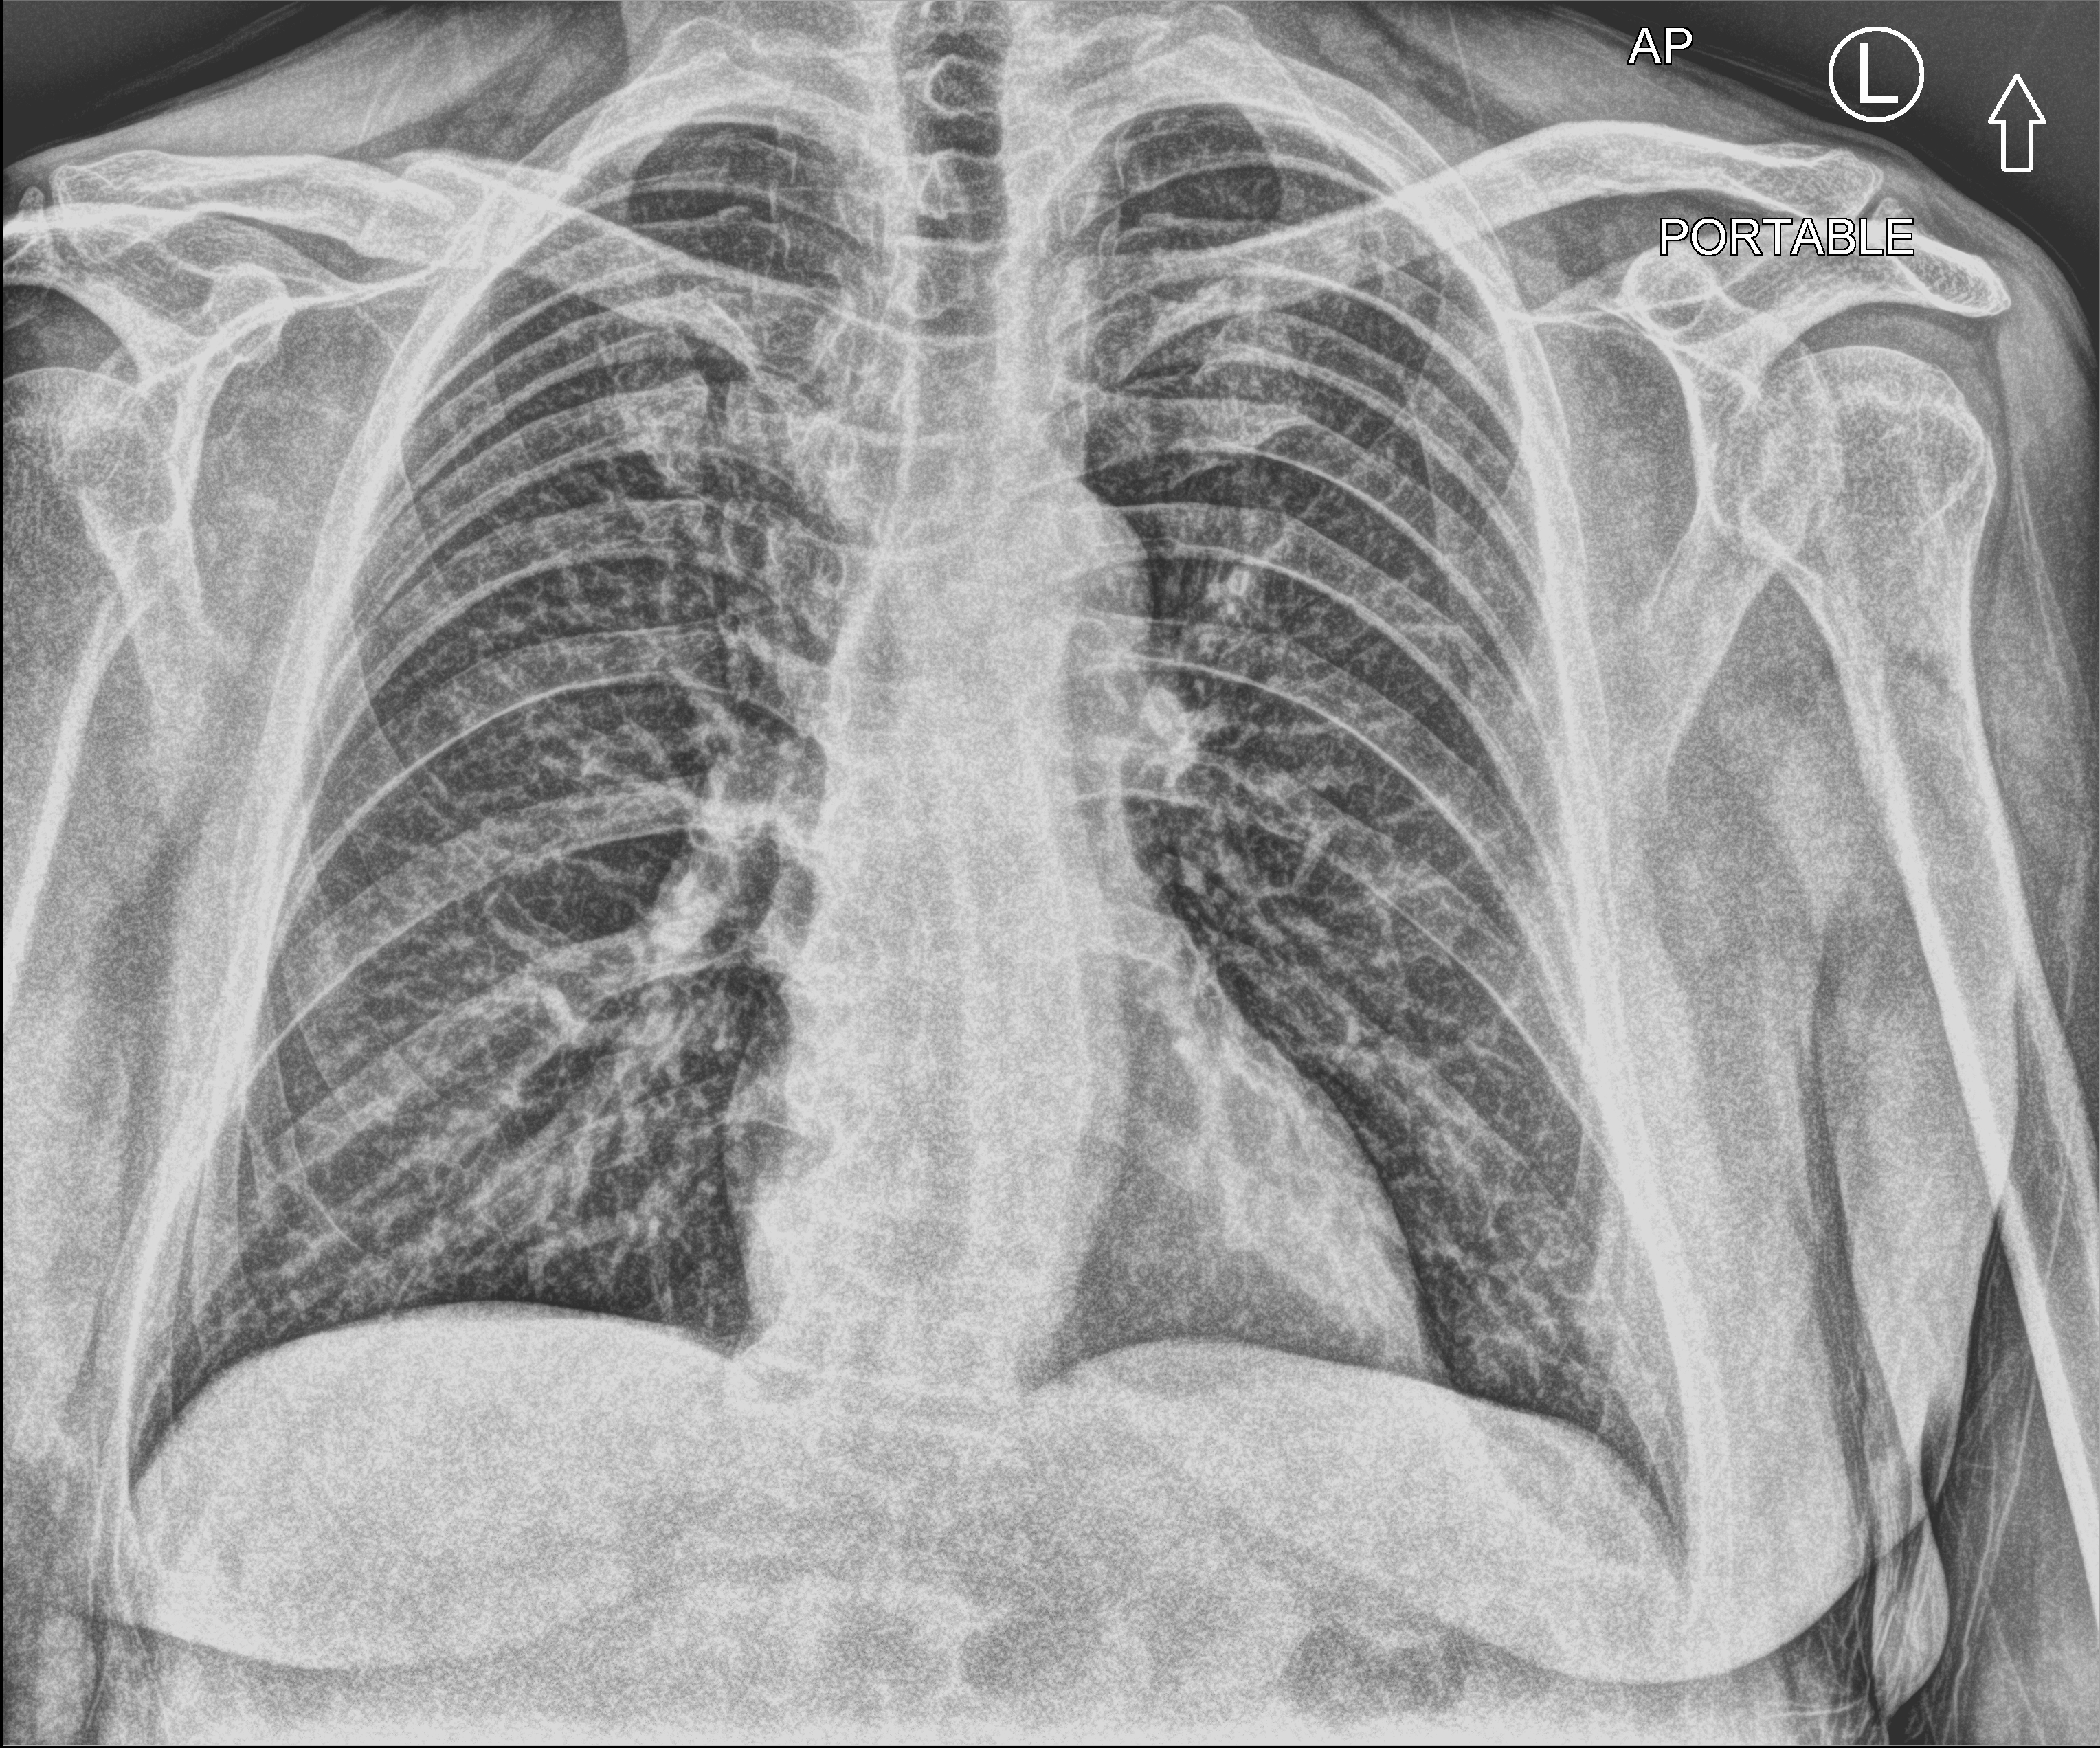
Portable chest radiograph, anteroposterior (AP) projection. Patient hospitalised with COVID-19; male, aged 60–74 years.
Admission-level facts for this patient (not findings on this image; timing relative to this image not recorded): smoking status (admission record): never; mechanically ventilated during this hospital stay: no; admitted to intensive care during this hospital stay: no.